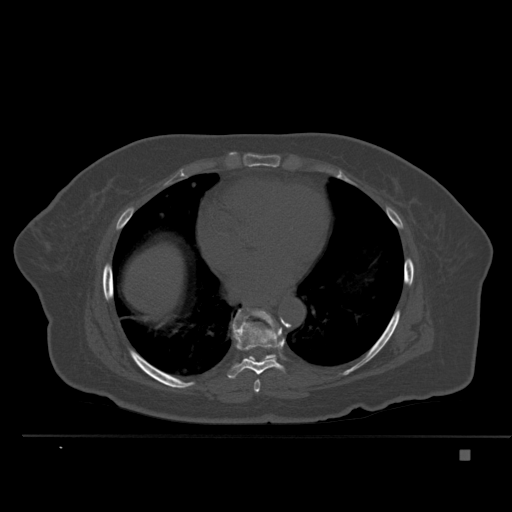
CT including the spine, one axial slice; position 310 of 477 along the scan axis; bone window (W 1800 / L 400 HU); 512 × 512 image matrix. Patient: female, 74 years. From the clinical record (not read from this slice): primary cancer: colon.
Outlined on this slice (semi-automatically segmented with operator editing):
- T7 vertebra: bounding box <254,380,260,393> (left, top, right, bottom; pixels)
- T8 vertebra: <228,310,285,379>
- T9 vertebra: <235,308,280,362>